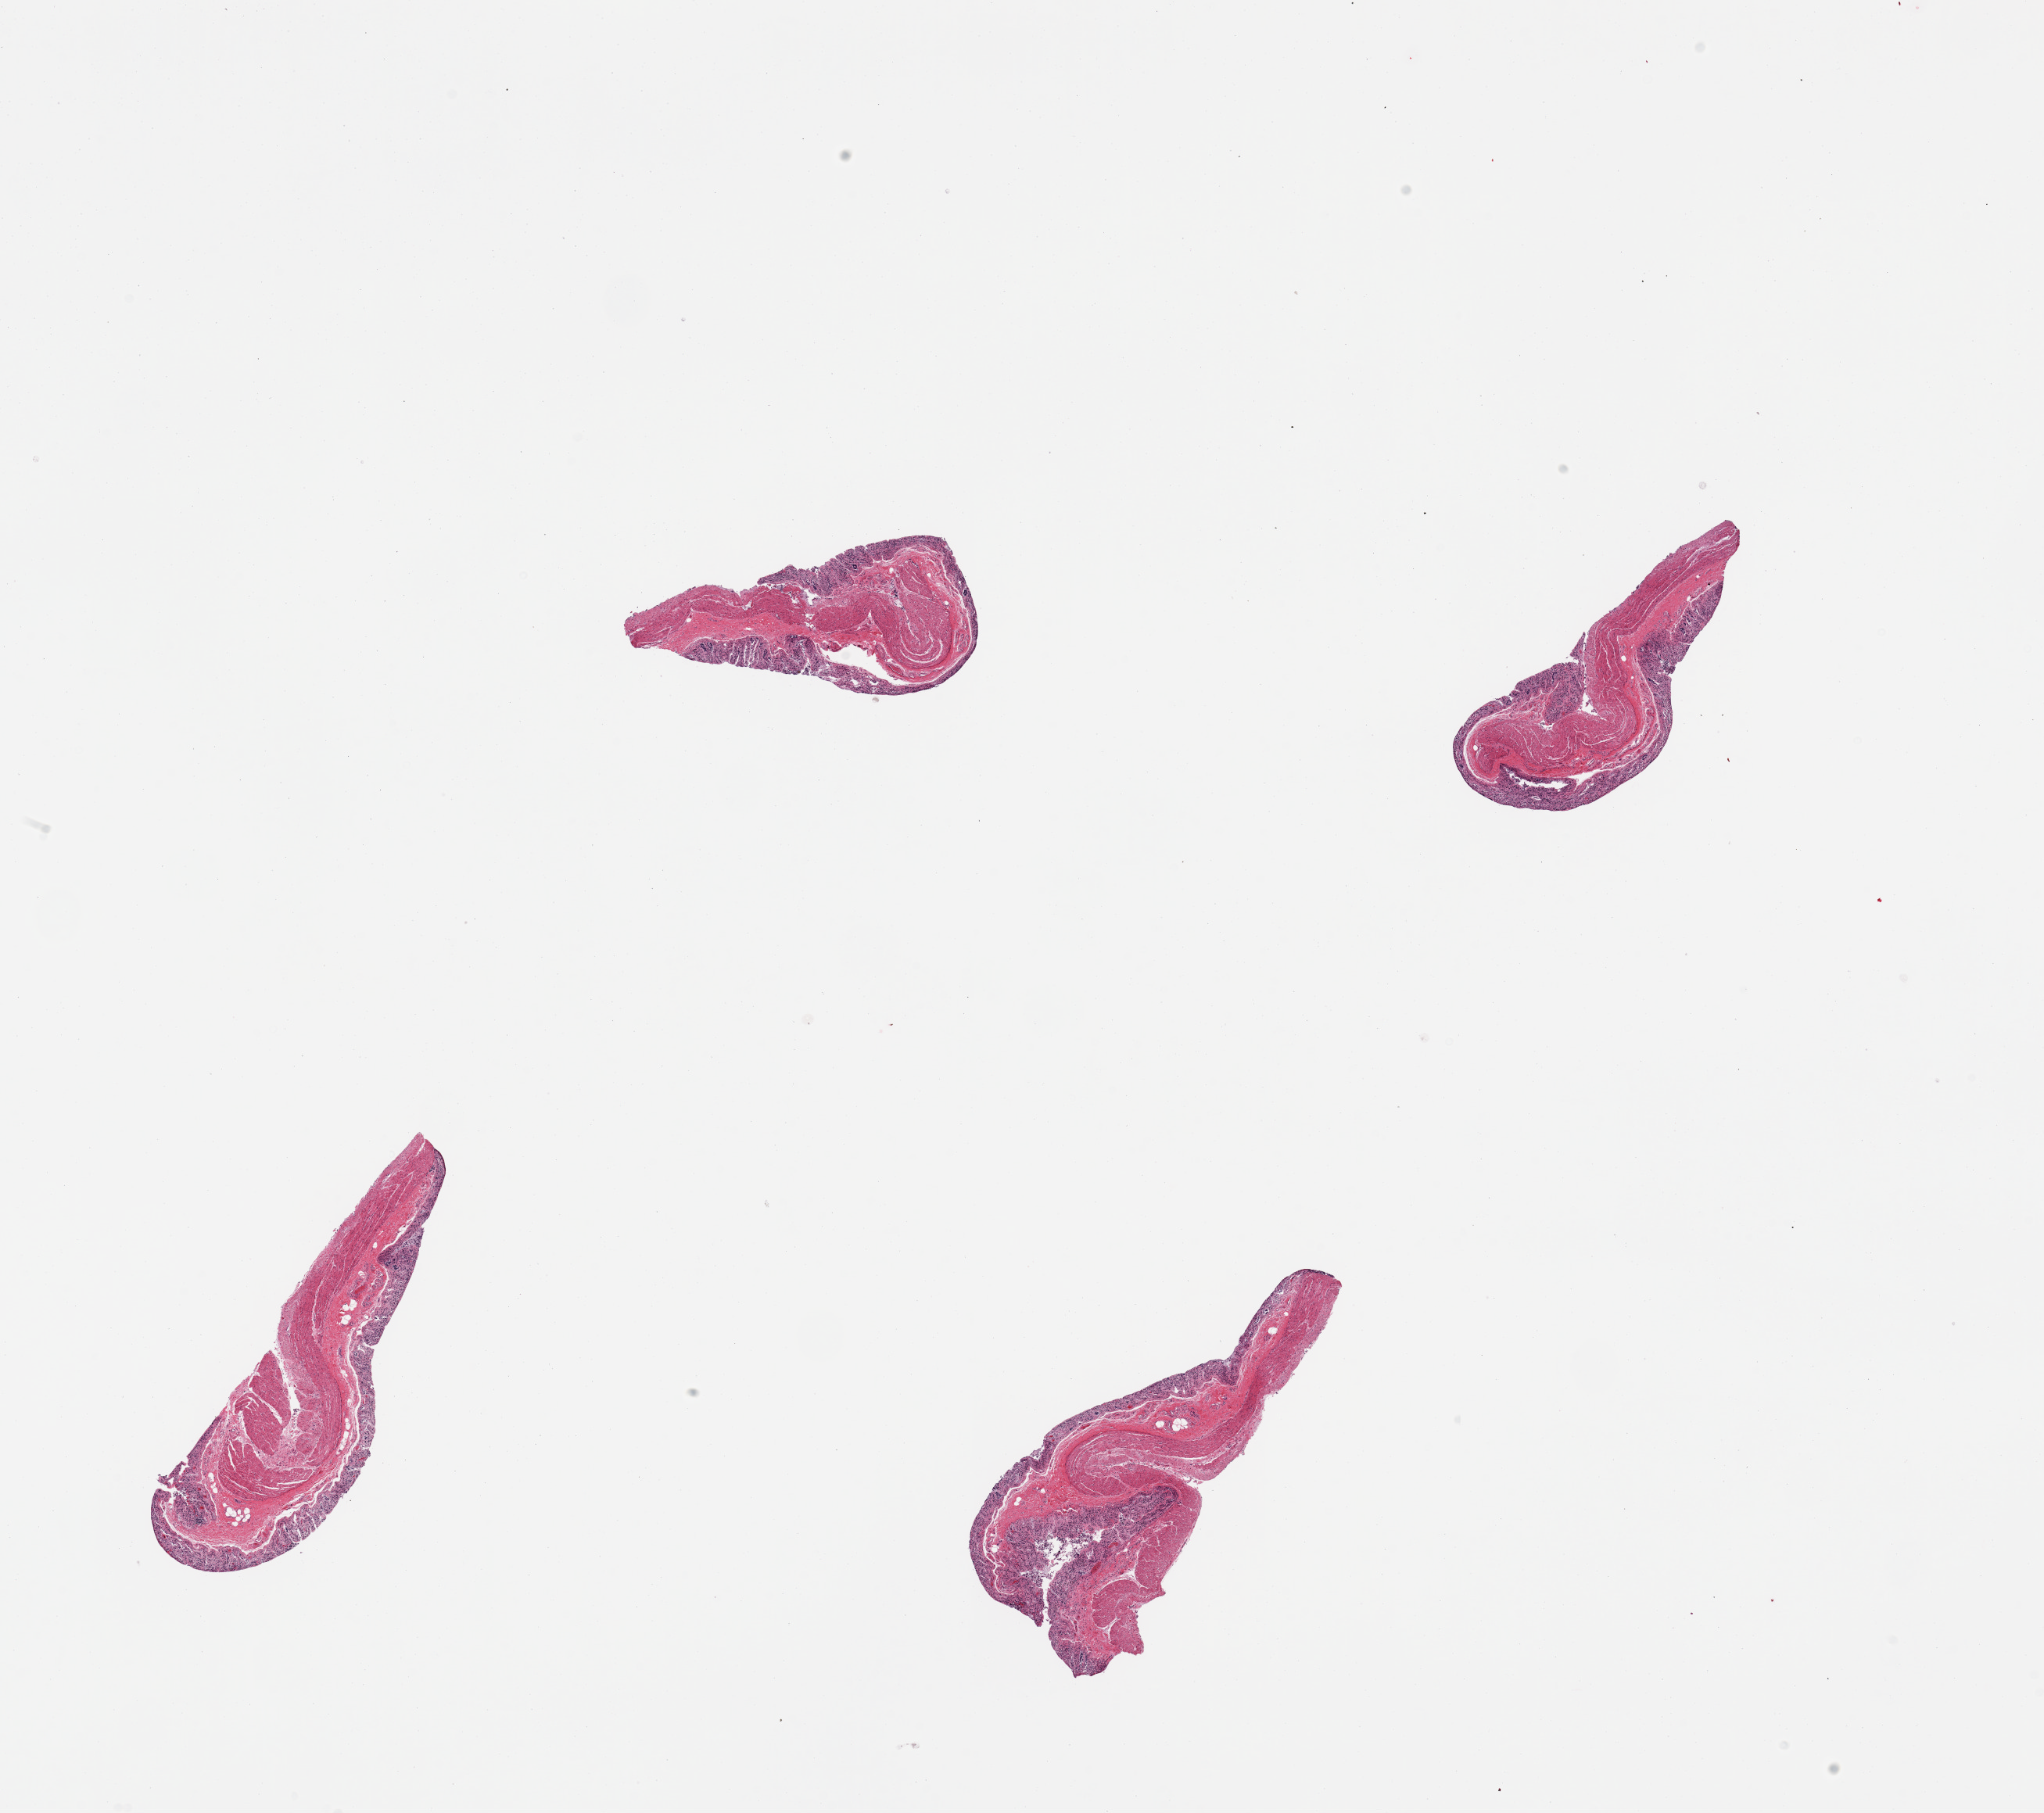
Haematoxylin and eosin whole-slide image, whole scanned area (about 20.7 x 18.3 mm, from a 20x scan) shown as a low-resolution overview, PAXgene-fixed paraffin-embedded (PFPE) section, section of transverse colon (target tissue), tissue donor sample. Donor sex: male.
- review note (as recorded): 4 pieces; completely autolyzed mucosa and preserved muscularis